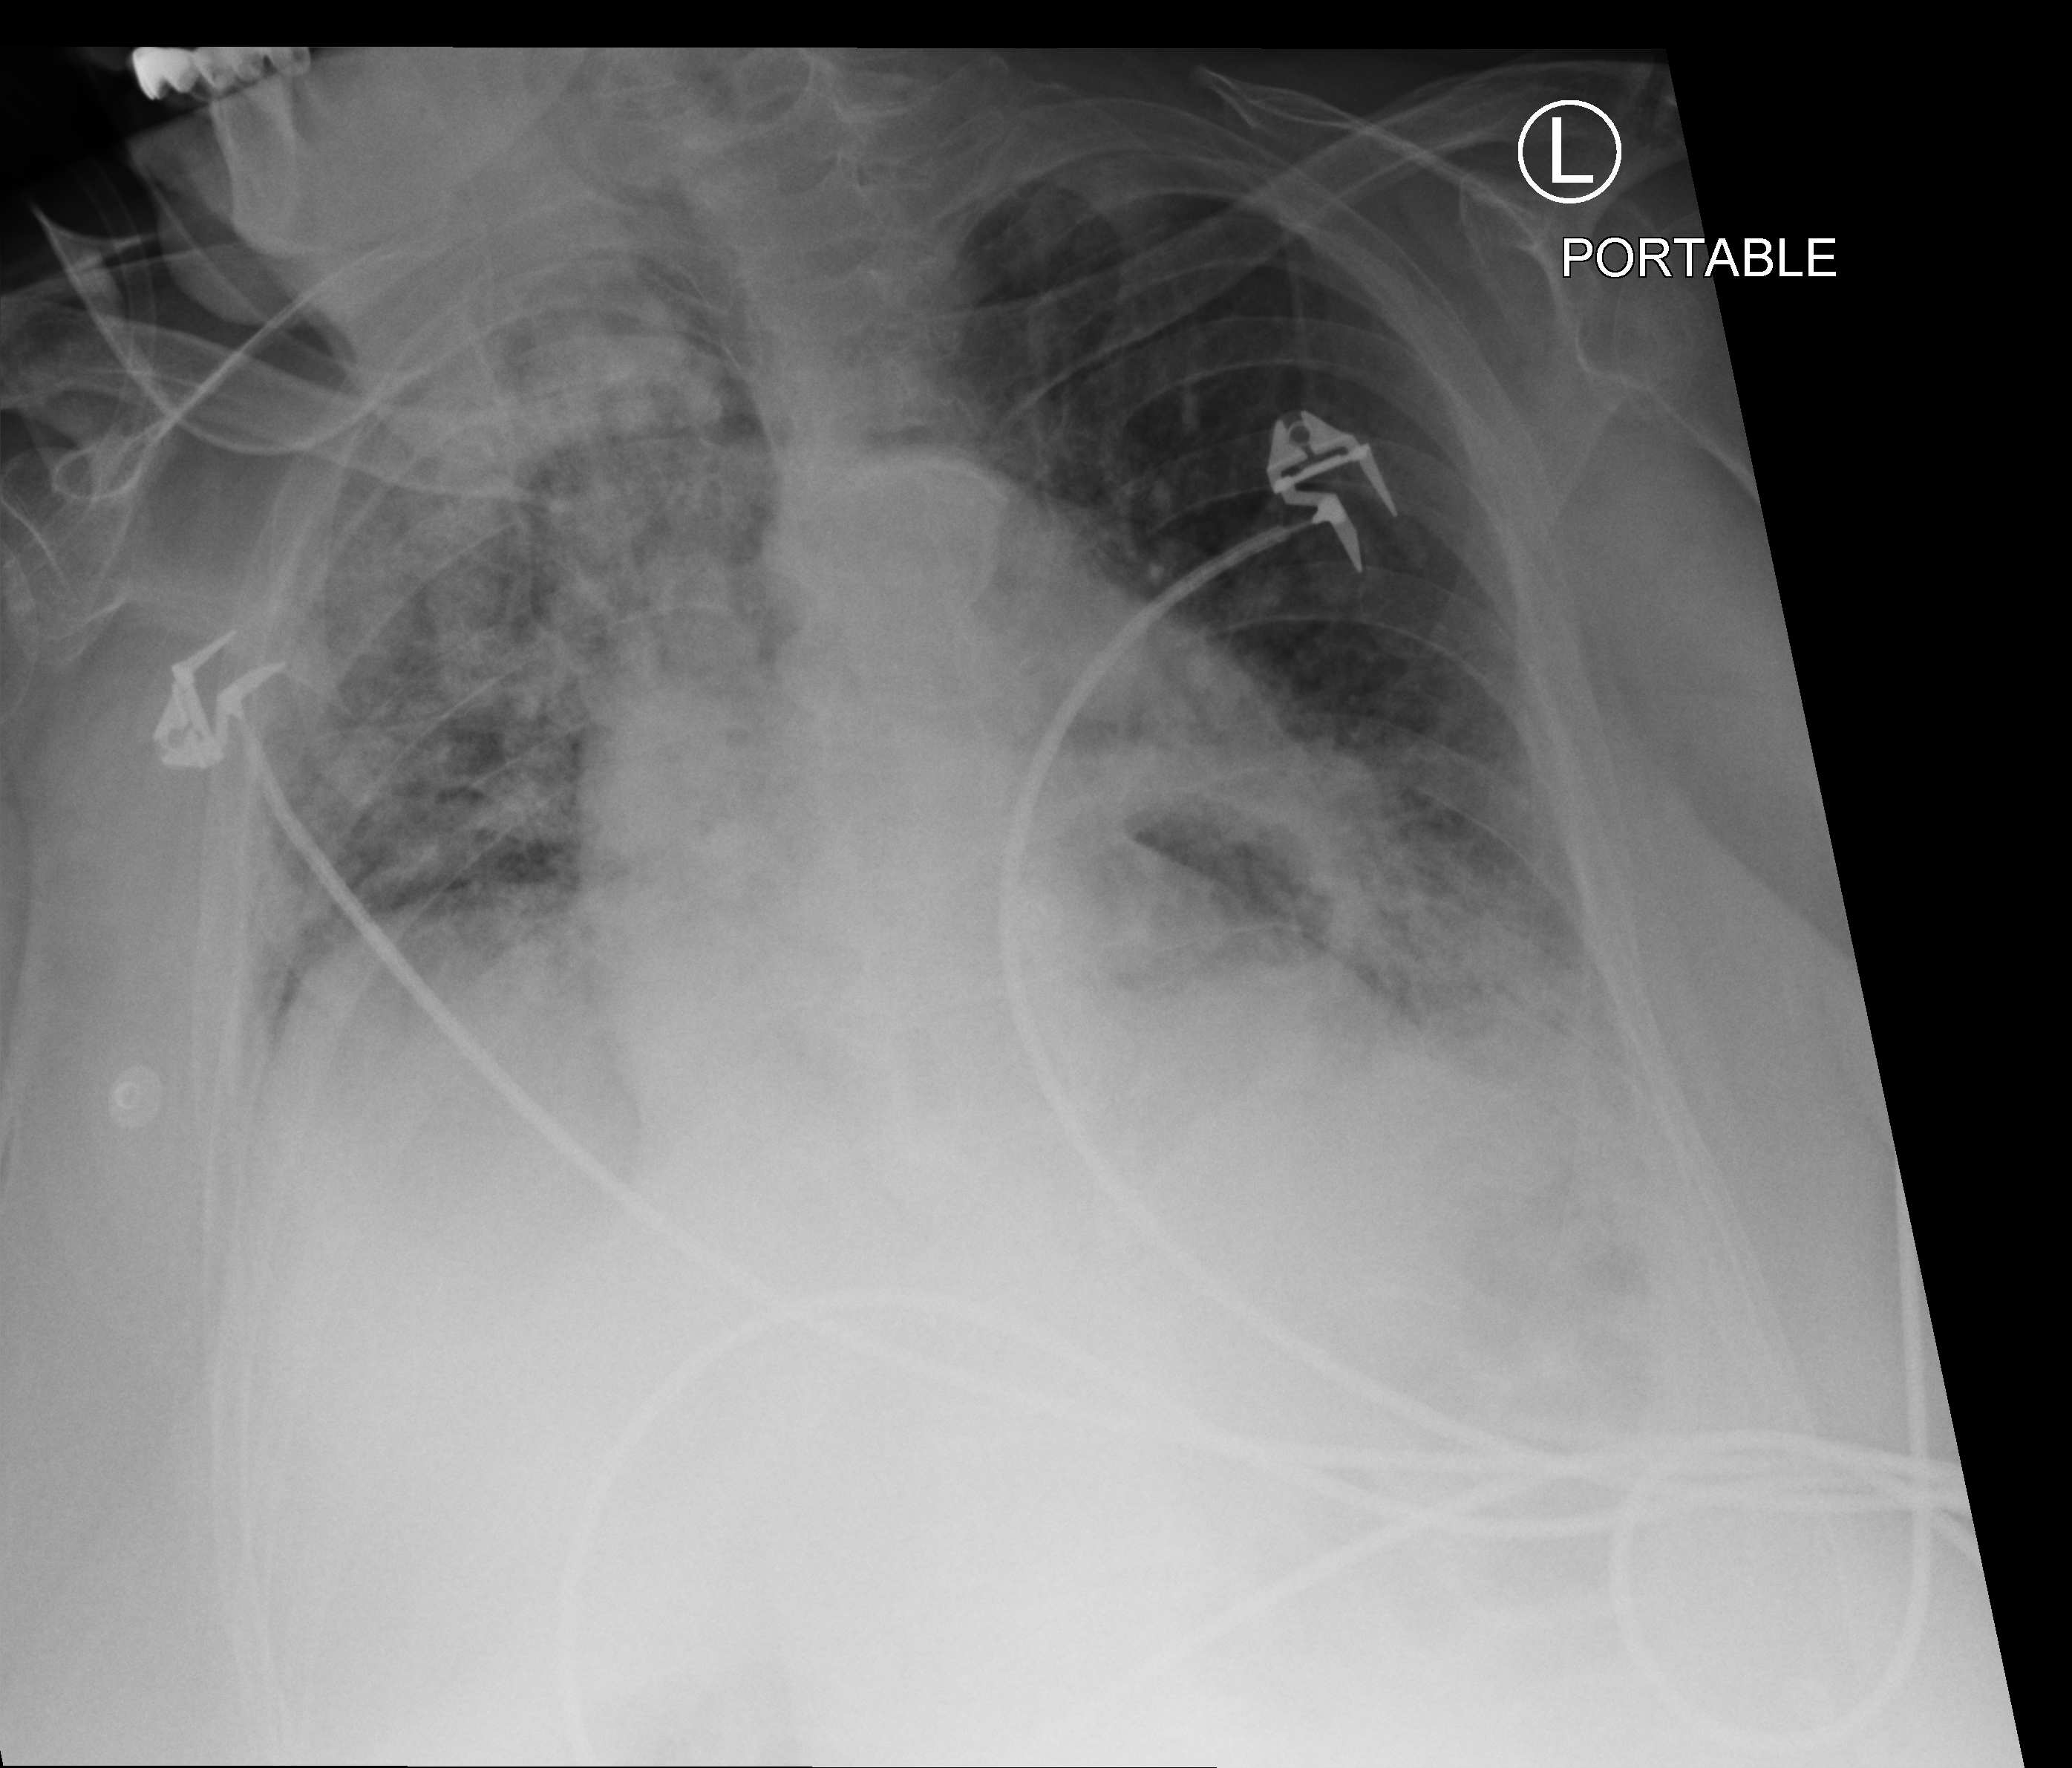
Portable chest radiograph, anteroposterior (AP) projection. Female patient hospitalised with COVID-19, age 75–90 years.
Admission-level facts for this patient (not findings on this image; timing relative to this image not recorded):
- chronic kidney disease (admission record): no